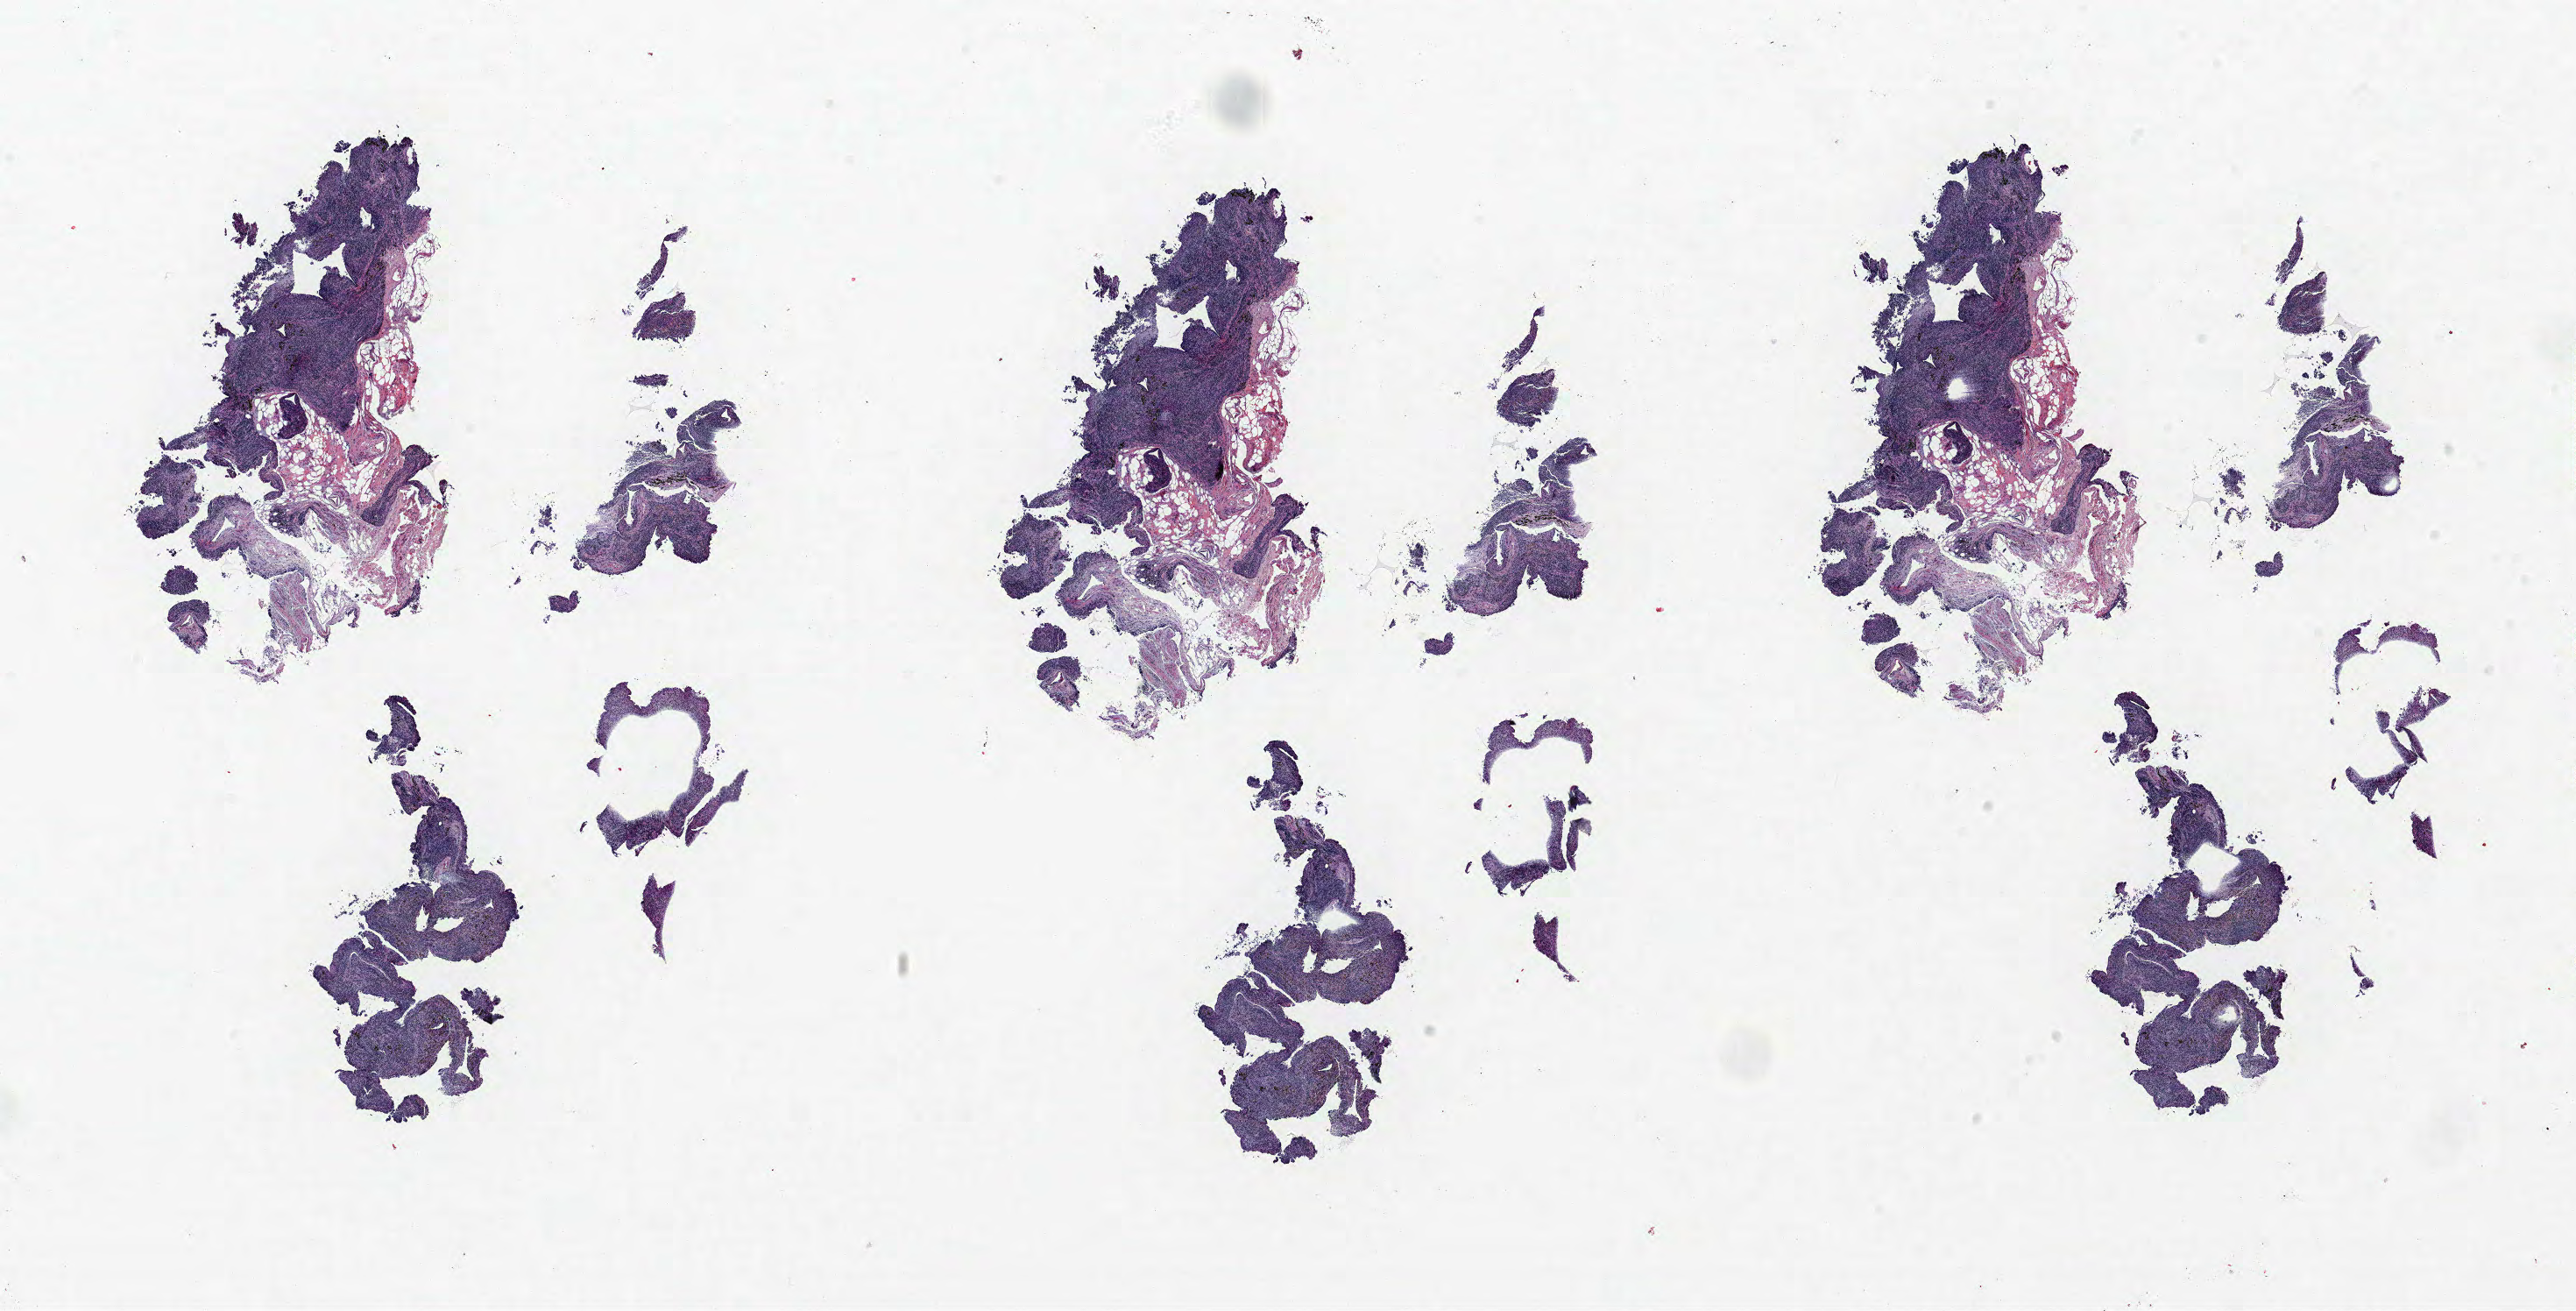
Whole-slide histology image, Hematoxylin and eosin (H&E) stained, shown as a low-resolution overview of the whole scanned area (about 23.5 x 12.0 mm). FFPE section. Lung. Female, age 70 at enrolment. Current smoker at enrolment.
* stage (AJCC 6th edition): IIIA
* participant's lung-cancer diagnosis: Non-small cell carcinoma
* tumour size (pathology): 12 mm
* primary tumour location (clinical record): right upper lobe
* ICD-O-3 topography: upper lobe of lung (C34.1)